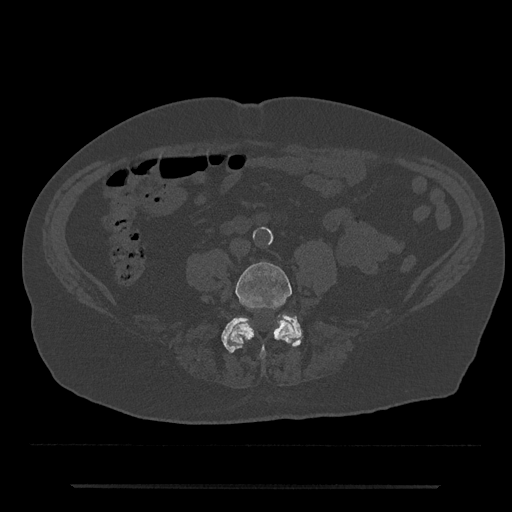
CT including the spine, one axial slice; slice 330 of 797 in the series (ordered by position); reconstruction kernel Br40s/3; 120 kVp; bone window (W 1800 / L 400 HU); 512 × 512 image matrix, field of view 434 × 434 mm. Patient: male, 80 years. From the clinical record (not read from this slice): primary cancer: prostate.
Structures marked on this image (semi-automatic segmentation, software-assisted and operator-edited):
- L4 vertebra: bounding box (x1, y1, x2, y2) in pixels: (227, 262, 297, 359)
- L5 vertebra: (221, 315, 302, 353)